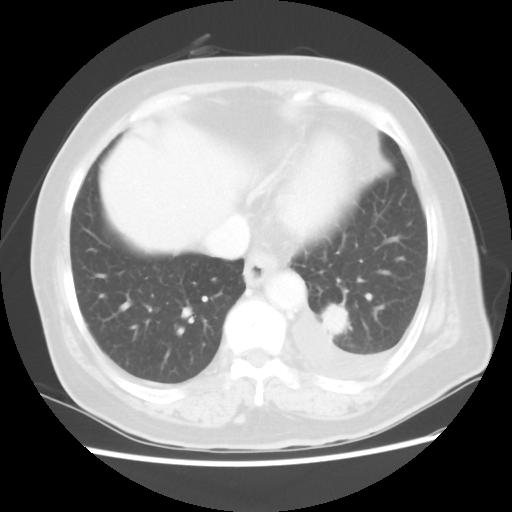
Chest CT, one axial slice. Position 14 of 80 along the scan axis. 100 kVp. Lung window (W 1500 / L -600 HU). 5 mm slice thickness. 512 × 512 image matrix, field of view 343 × 343 mm. Female patient, age 68 years. From the clinical record (not read from this slice): clinical TNM (as recorded): T1c N0 M1.
Outlined on this slice (rectangle marked by the reading radiologist):
- lung tumour (recorded histology: adenocarcinoma): bounding box <316,304,355,339> (left, top, right, bottom; pixels)